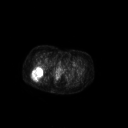
FDG PET of an extremity soft-tissue mass (from a PET/CT study), one axial slice. Position 55 of 267 along the scan axis. 3.27 mm slice thickness. 128 × 128 image matrix, field of view 700 × 700 mm. Female patient, age 70 years. From the clinical record (not read from this slice): histological type: synovial sarcoma; grade: intermediate; site of the primary tumour: right buttock.
Structures marked on this image (expert contour drawn on MRI and transferred to this co-registered scan by the dataset authors):
- gross tumour volume including surrounding oedema: box from (x=31, y=65) to (x=44, y=82) px
- gross tumour volume (mass): (x=31, y=65)–(x=44, y=80)